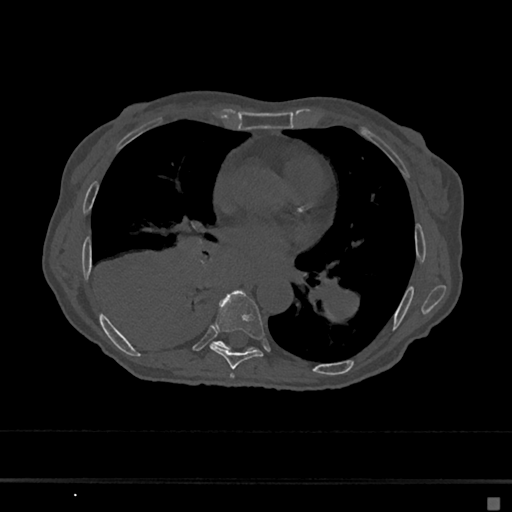
CT including the spine, one axial slice. Slice 360 of 797 in the series (ordered by position). Reconstruction kernel Br40s/3. Bone window (W 1800 / L 400 HU). 0.5 mm slice thickness. 512 × 512 image matrix. Patient: female, 68 years. Case-level facts recorded for this patient, not image findings: primary cancer: renal.
Annotated regions visible in this slice (semi-automatic segmentation, software-assisted and operator-edited):
- T6 vertebra: bounding box [x1, y1, x2, y2] px = [230, 373, 235, 379]
- T7 vertebra: [210, 291, 264, 369]
- T8 vertebra: [214, 341, 254, 351]